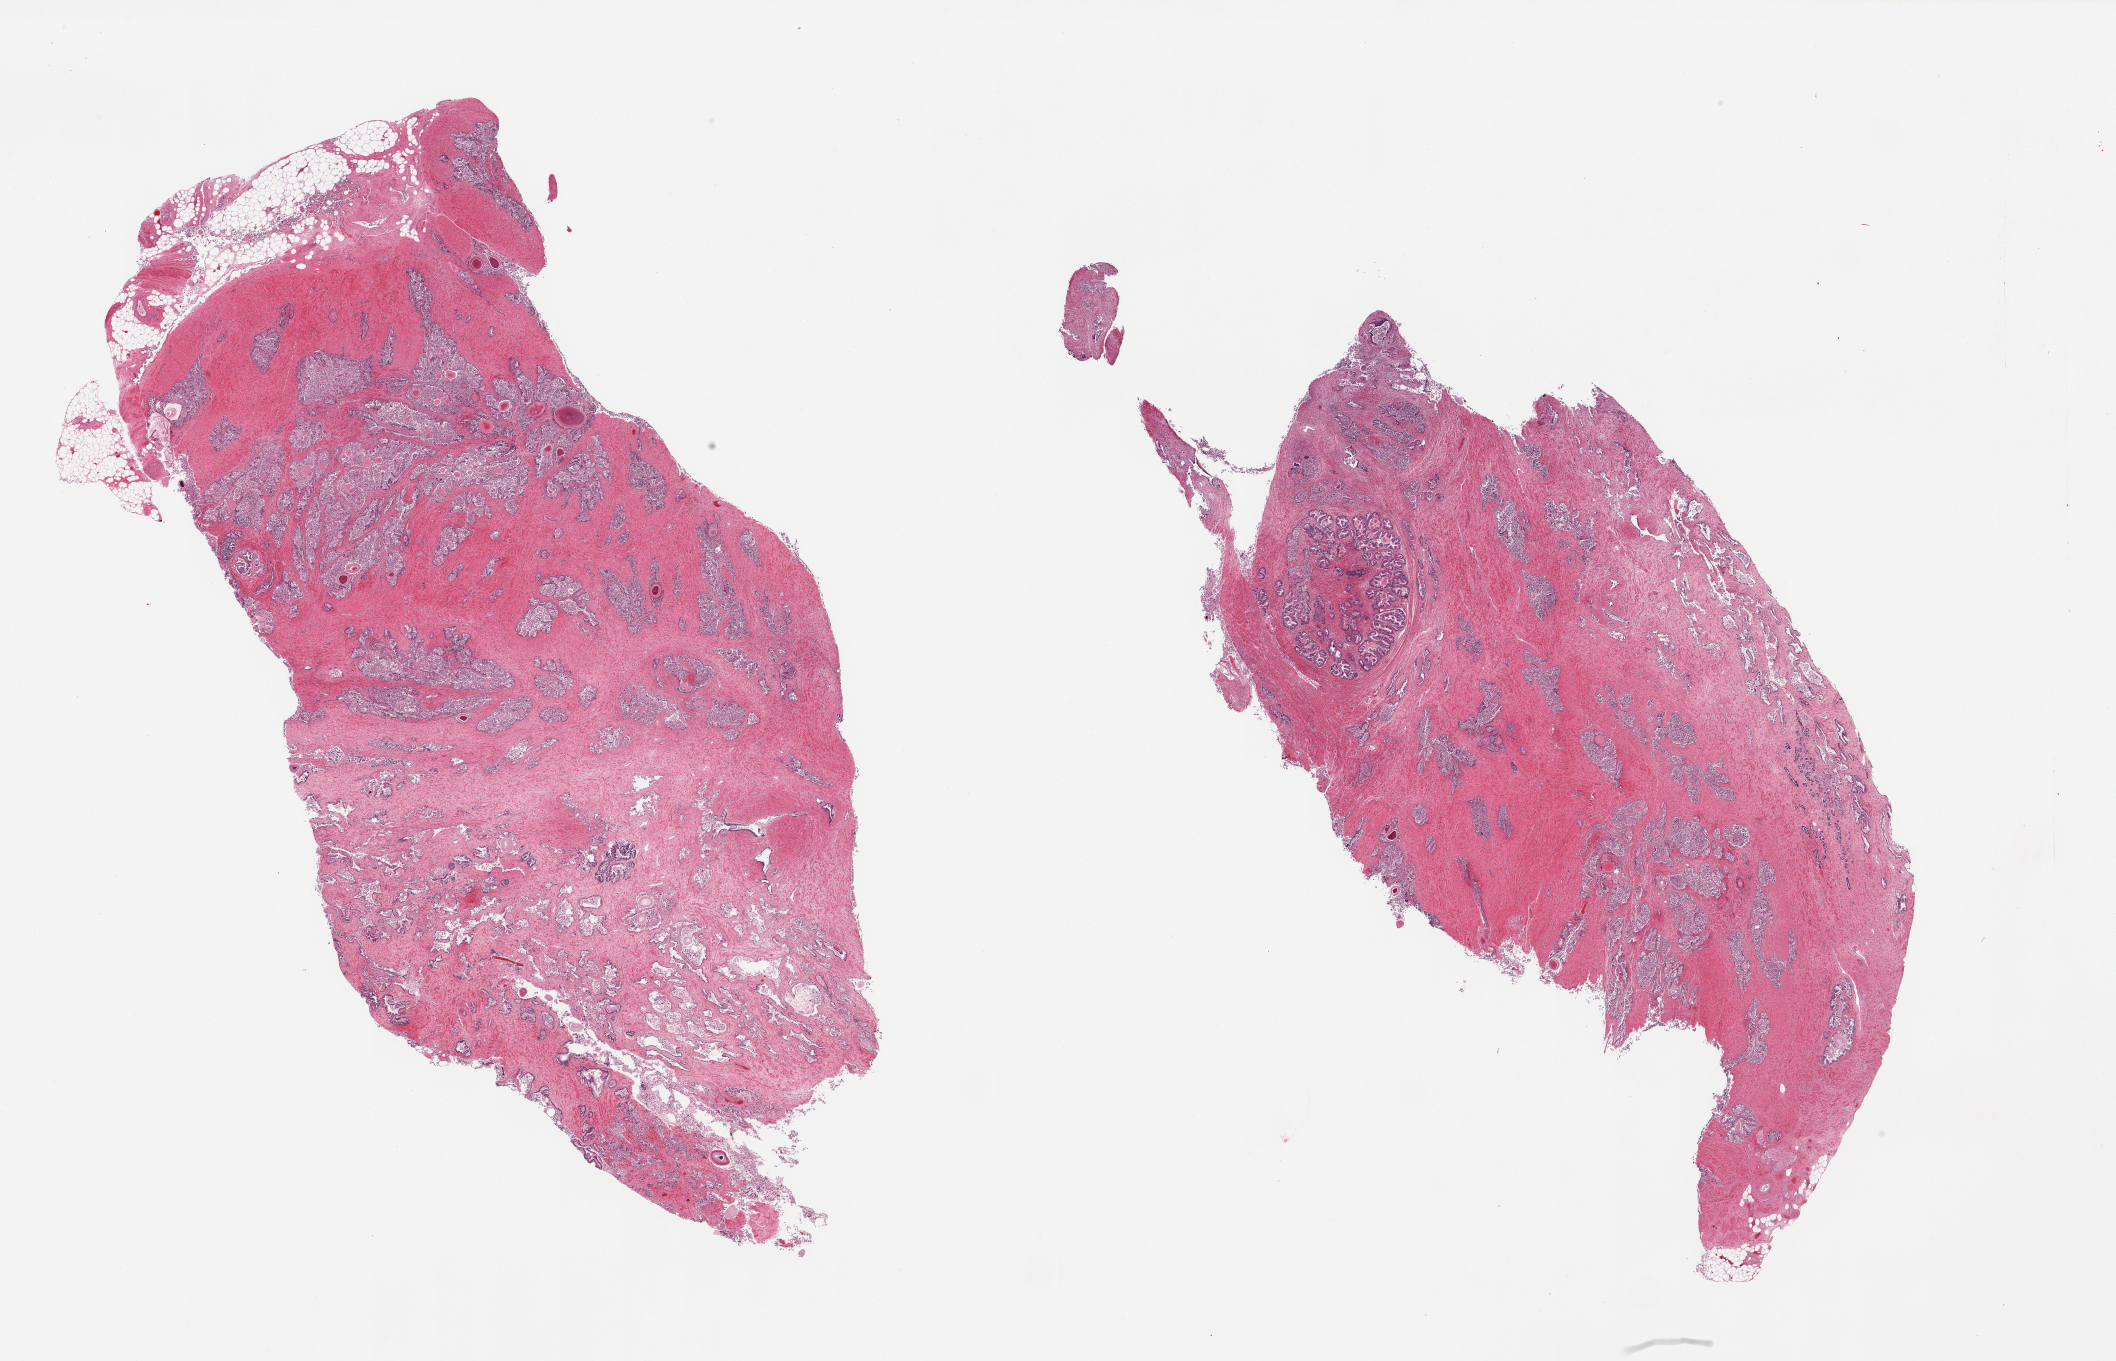
H&E whole-slide image, a low-resolution overview of the entire scanned area, about 33.5 x 21.5 mm (from a 20x scan), PAXgene-fixed, paraffin-embedded tissue, section of prostate (target tissue), donor tissue sample. Donor: male.
Reviewer comment on this tissue sample: 2 pieces, advanced glandular mucosal autolysis.